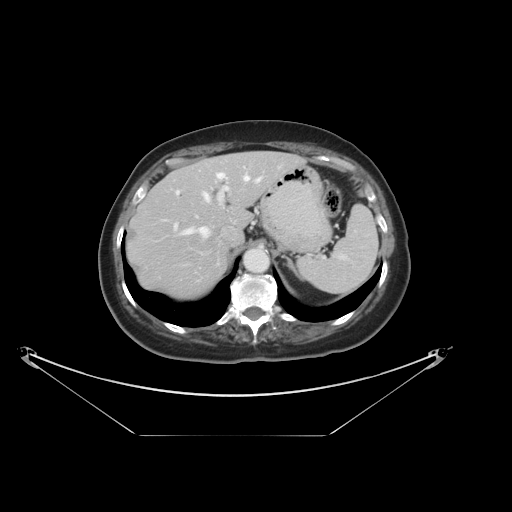
Contrast-enhanced abdominal CT, one axial slice; position 26 of 36 along the scan axis; 120 kVp; soft-tissue window (W 400 / L 40 HU); 5 mm slice thickness; 512 × 512 image matrix, field of view 500 × 500 mm. Female patient, age 70 years. Case-level facts recorded for this patient, not image findings: diagnosis: colorectal cancer liver metastases, imaged before liver resection; multiple liver metastases: no; largest metastasis: 2.5 cm.
Outlined on this slice (expert manual segmentation):
- hepatic veins: bounding box (x1, y1, x2, y2) in pixels: (182, 173, 261, 235)
- liver: (127, 152, 304, 298)
- planned liver remnant (the part of the liver to remain after resection): (127, 152, 304, 299)
- portal vein (with intrahepatic branches): (173, 169, 230, 239)